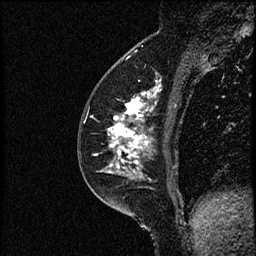
Breast MRI (dynamic contrast-enhanced), one sagittal slice. Slice 30 of 52 in the series (ordered by position). Dynamic contrast-enhanced study with each time point stored as its own series, time point 2 of 3 at this slice position (early post-contrast, ordered by acquisition time). 1.5 T. TE 4.2 ms, TR 17.6 ms. 2 mm slice thickness. 256 × 256 image matrix. Patient: female, 49 years. From the clinical record (not read from this slice): setting: breast cancer imaged before/during neoadjuvant chemotherapy; receptor status: HER2-positive.
Annotated regions visible in this slice (semi-automatically segmented with operator editing):
- analysis volume of interest (the breast-tissue region the enhancement analysis was run in; not a lesion): bounding box <85,65,182,175> (left, top, right, bottom; pixels)
- tumour enhancement mask (voxels above the 100 % enhancement threshold inside the analysis volume of interest): <108,87,160,175>